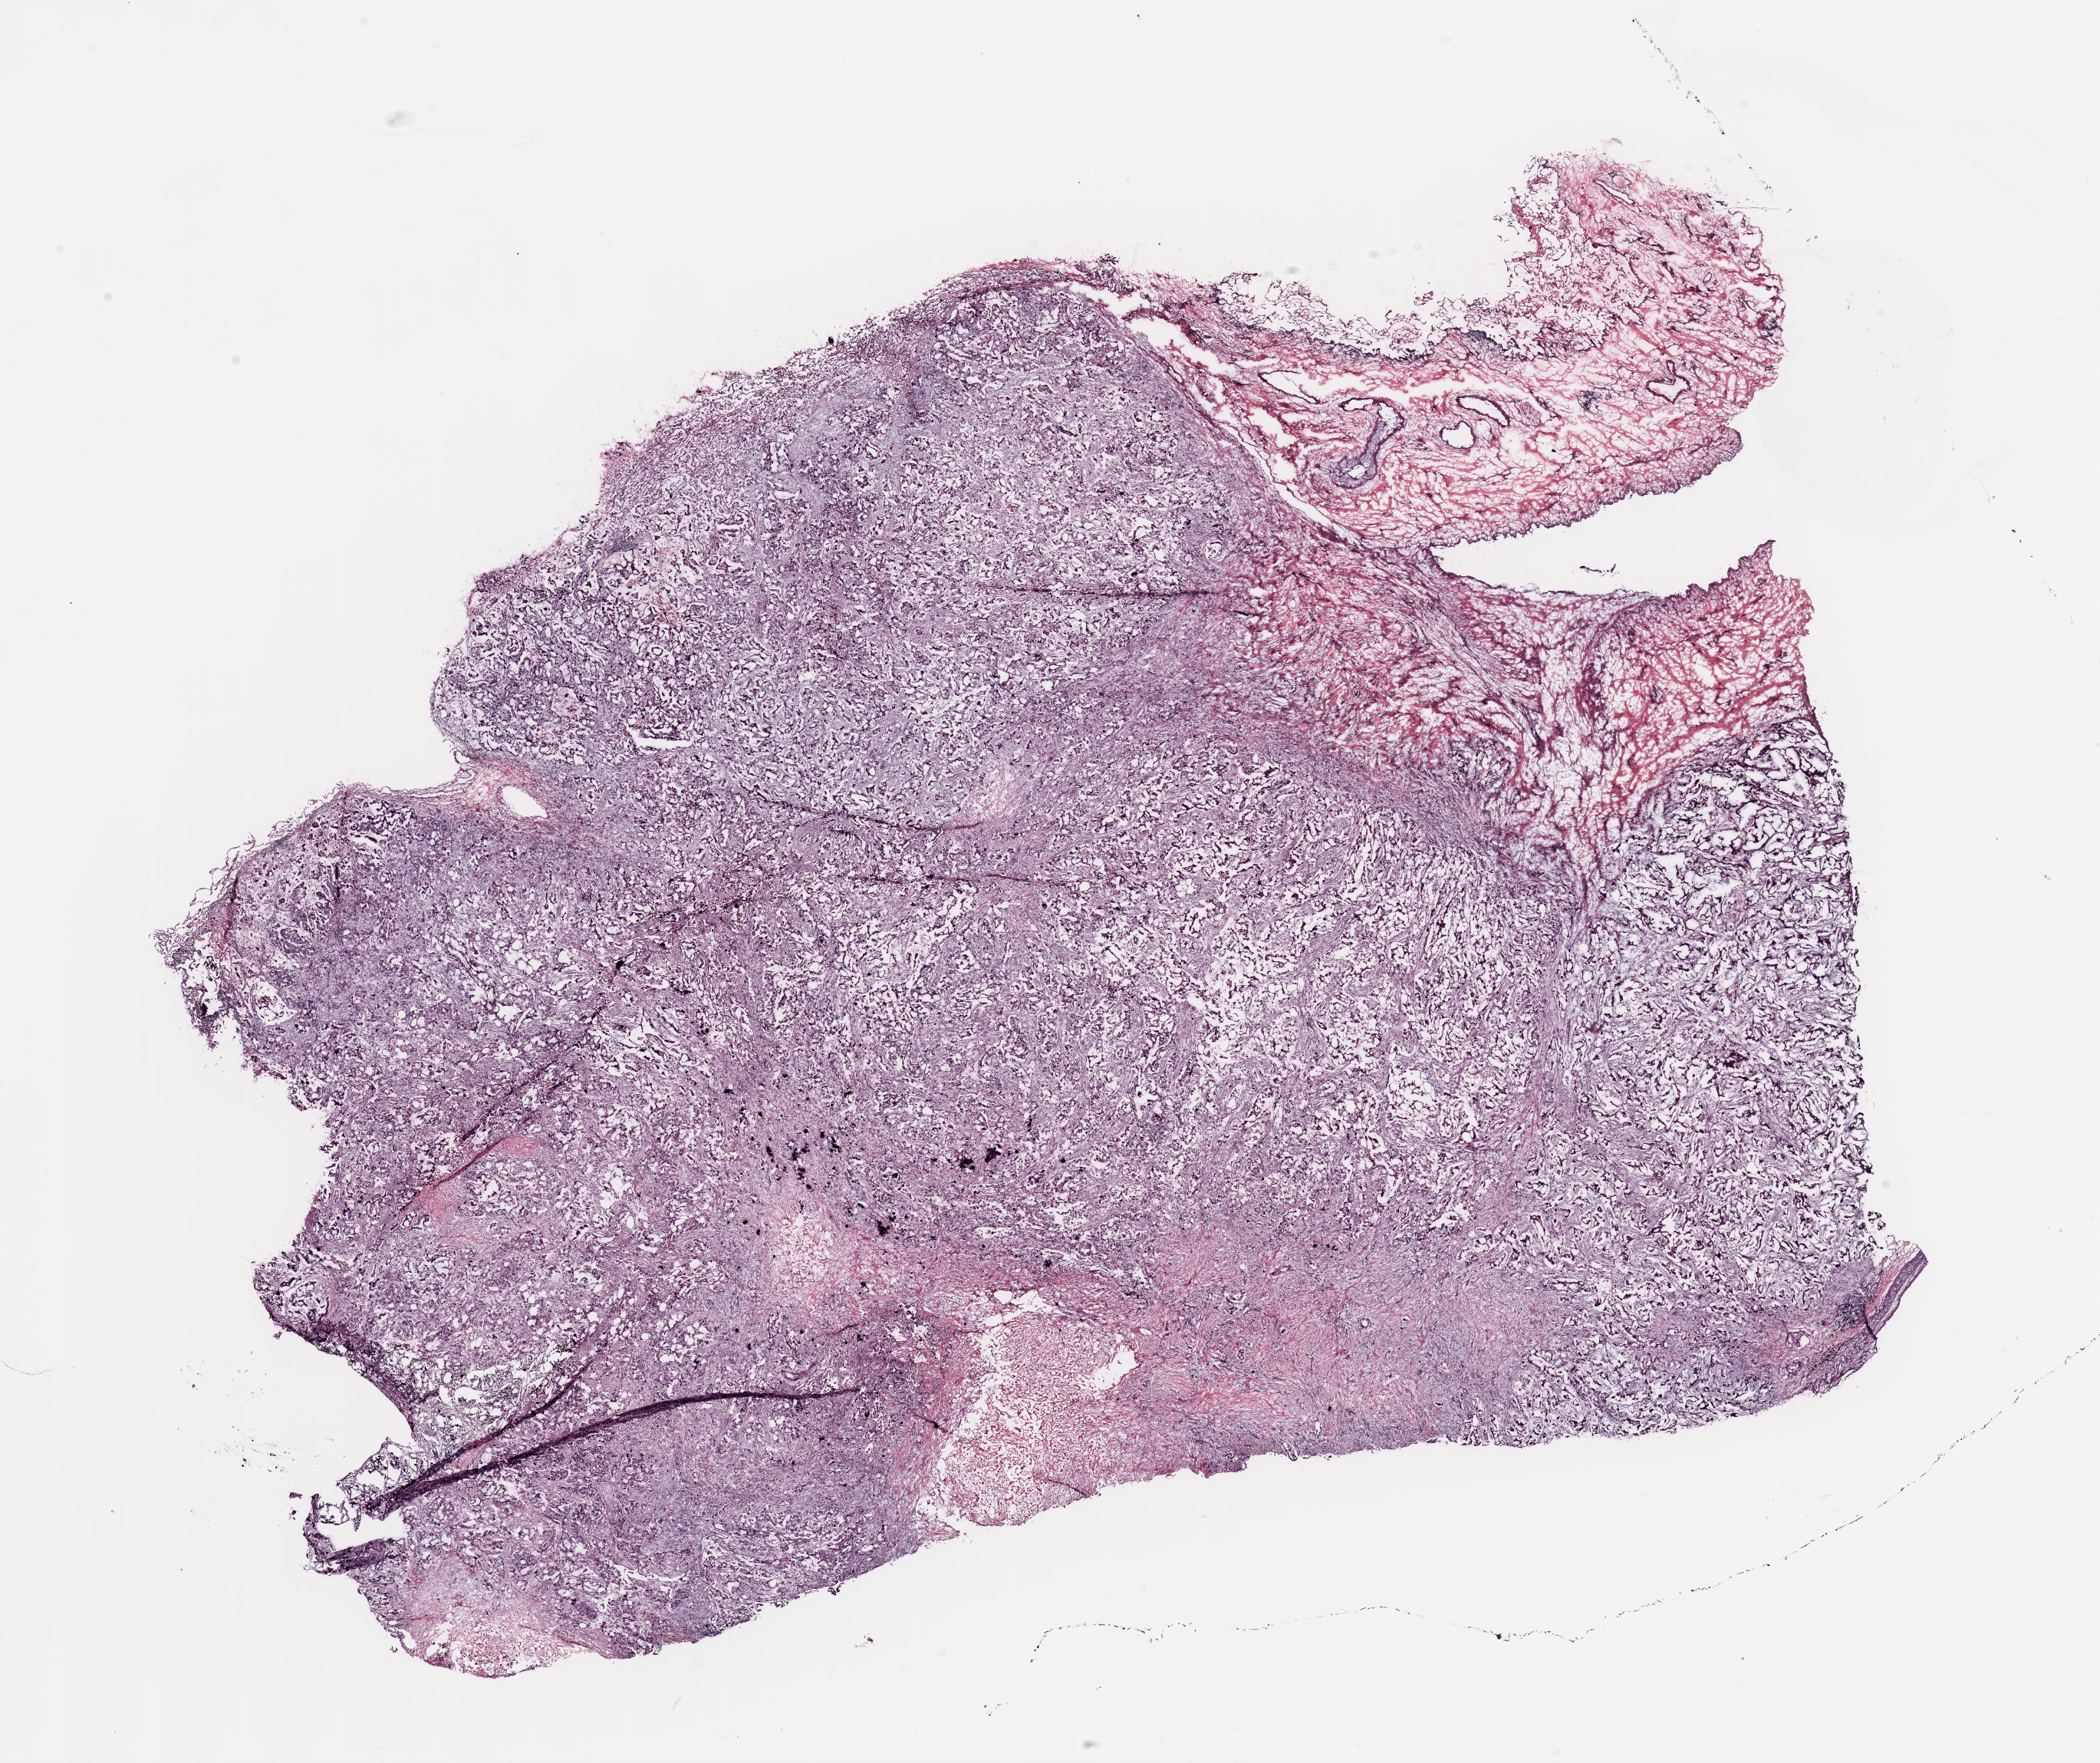
Digitized H&E-stained tissue section (whole slide), whole scanned area (about 21.7 x 18.2 mm, slide scanned at 20x) shown as a low-resolution overview, tumour tissue sample, sampled site: lung. Patient: male, age 59 years. Histologic grade: GX (grade cannot be assessed). Pathologist review of this section (percent, as recorded): tumour nuclei 70%, necrosis 10%.
Diagnosis: Adenocarcinoma, NOS. AJCC pathologic stage: IIIA.